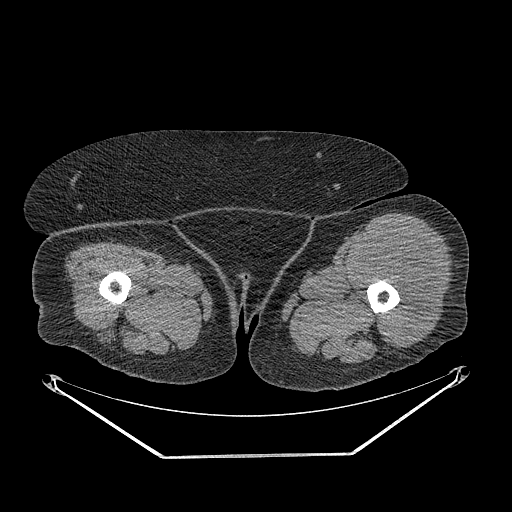
CT of an extremity soft-tissue mass (from a PET/CT study), one axial slice; soft-tissue window (W 400 / L 40 HU); 3.75 mm slice thickness; 512 × 512 image matrix, field of view 500 × 500 mm. Female patient. Case-level facts recorded for this patient, not image findings: histological type: undifferentiated – high grade; grade: high; site of the primary tumour: left thigh.
Outlined on this slice (expert contour drawn on MRI and transferred to this co-registered scan by the dataset authors):
- gross tumour volume including surrounding oedema: bounding box (x1, y1, x2, y2) in pixels: (354, 233, 437, 350)
- gross tumour volume (mass): (356, 242, 435, 348)